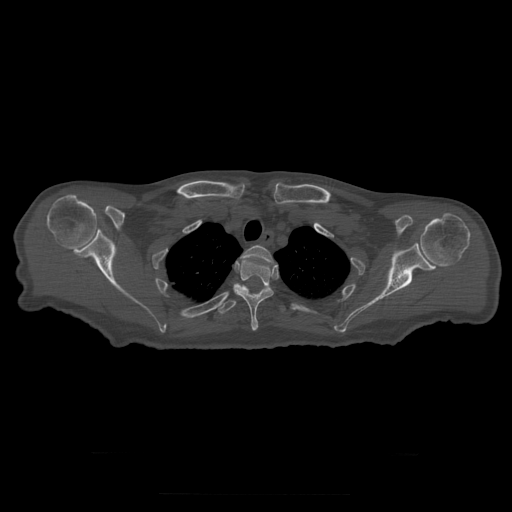
CT including the spine, one axial slice; slice 257 of 397 in the series (ordered by position); reconstruction kernel STANDARD; 120 kVp; bone window (W 1800 / L 400 HU); 1.25 mm slice thickness; 512 × 512 image matrix. Patient age 73 years. Case-level facts recorded for this patient, not image findings: primary cancer: prostate.
Structures marked on this image (semi-automatically segmented with operator editing):
- T2 vertebra: bounding box <241,245,276,266> (left, top, right, bottom; pixels)
- T3 vertebra: <234,259,274,331>
- T4 vertebra: <218,283,286,315>